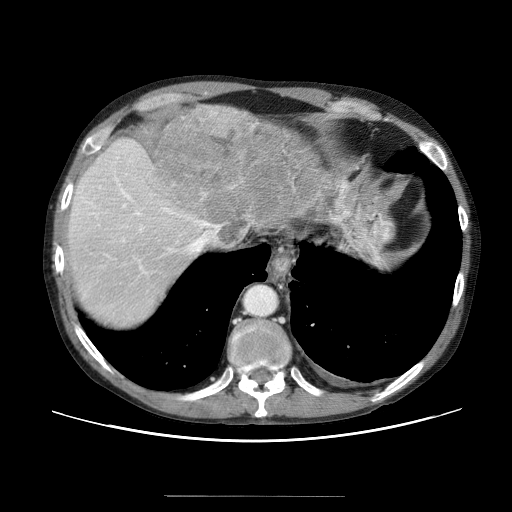
Contrast-enhanced abdominal CT (liver protocol), one axial slice. Slice 52 of 69 in the series (ordered by position). Soft-tissue window (W 400 / L 40 HU). 2.5 mm slice thickness. 512 × 512 image matrix. Case-level facts recorded for this patient, not image findings: diagnosis: hepatocellular carcinoma (patient treated with transarterial chemoembolisation; whether this scan precedes or follows treatment is not stated here); TNM stage (as recorded): Stage-IVB; Child-Pugh class: B; tumour nodularity: multinodular.
Structures marked on this image (semi-automatic segmentation, software-assisted and operator-edited):
- liver parenchyma outside the tumour (the mass and vessels are separate outlines, so this box may not span the whole liver): bounding box [x1, y1, x2, y2] px = [64, 104, 360, 336]
- mass: [147, 103, 334, 246]
- liver vessels: [95, 171, 177, 262]